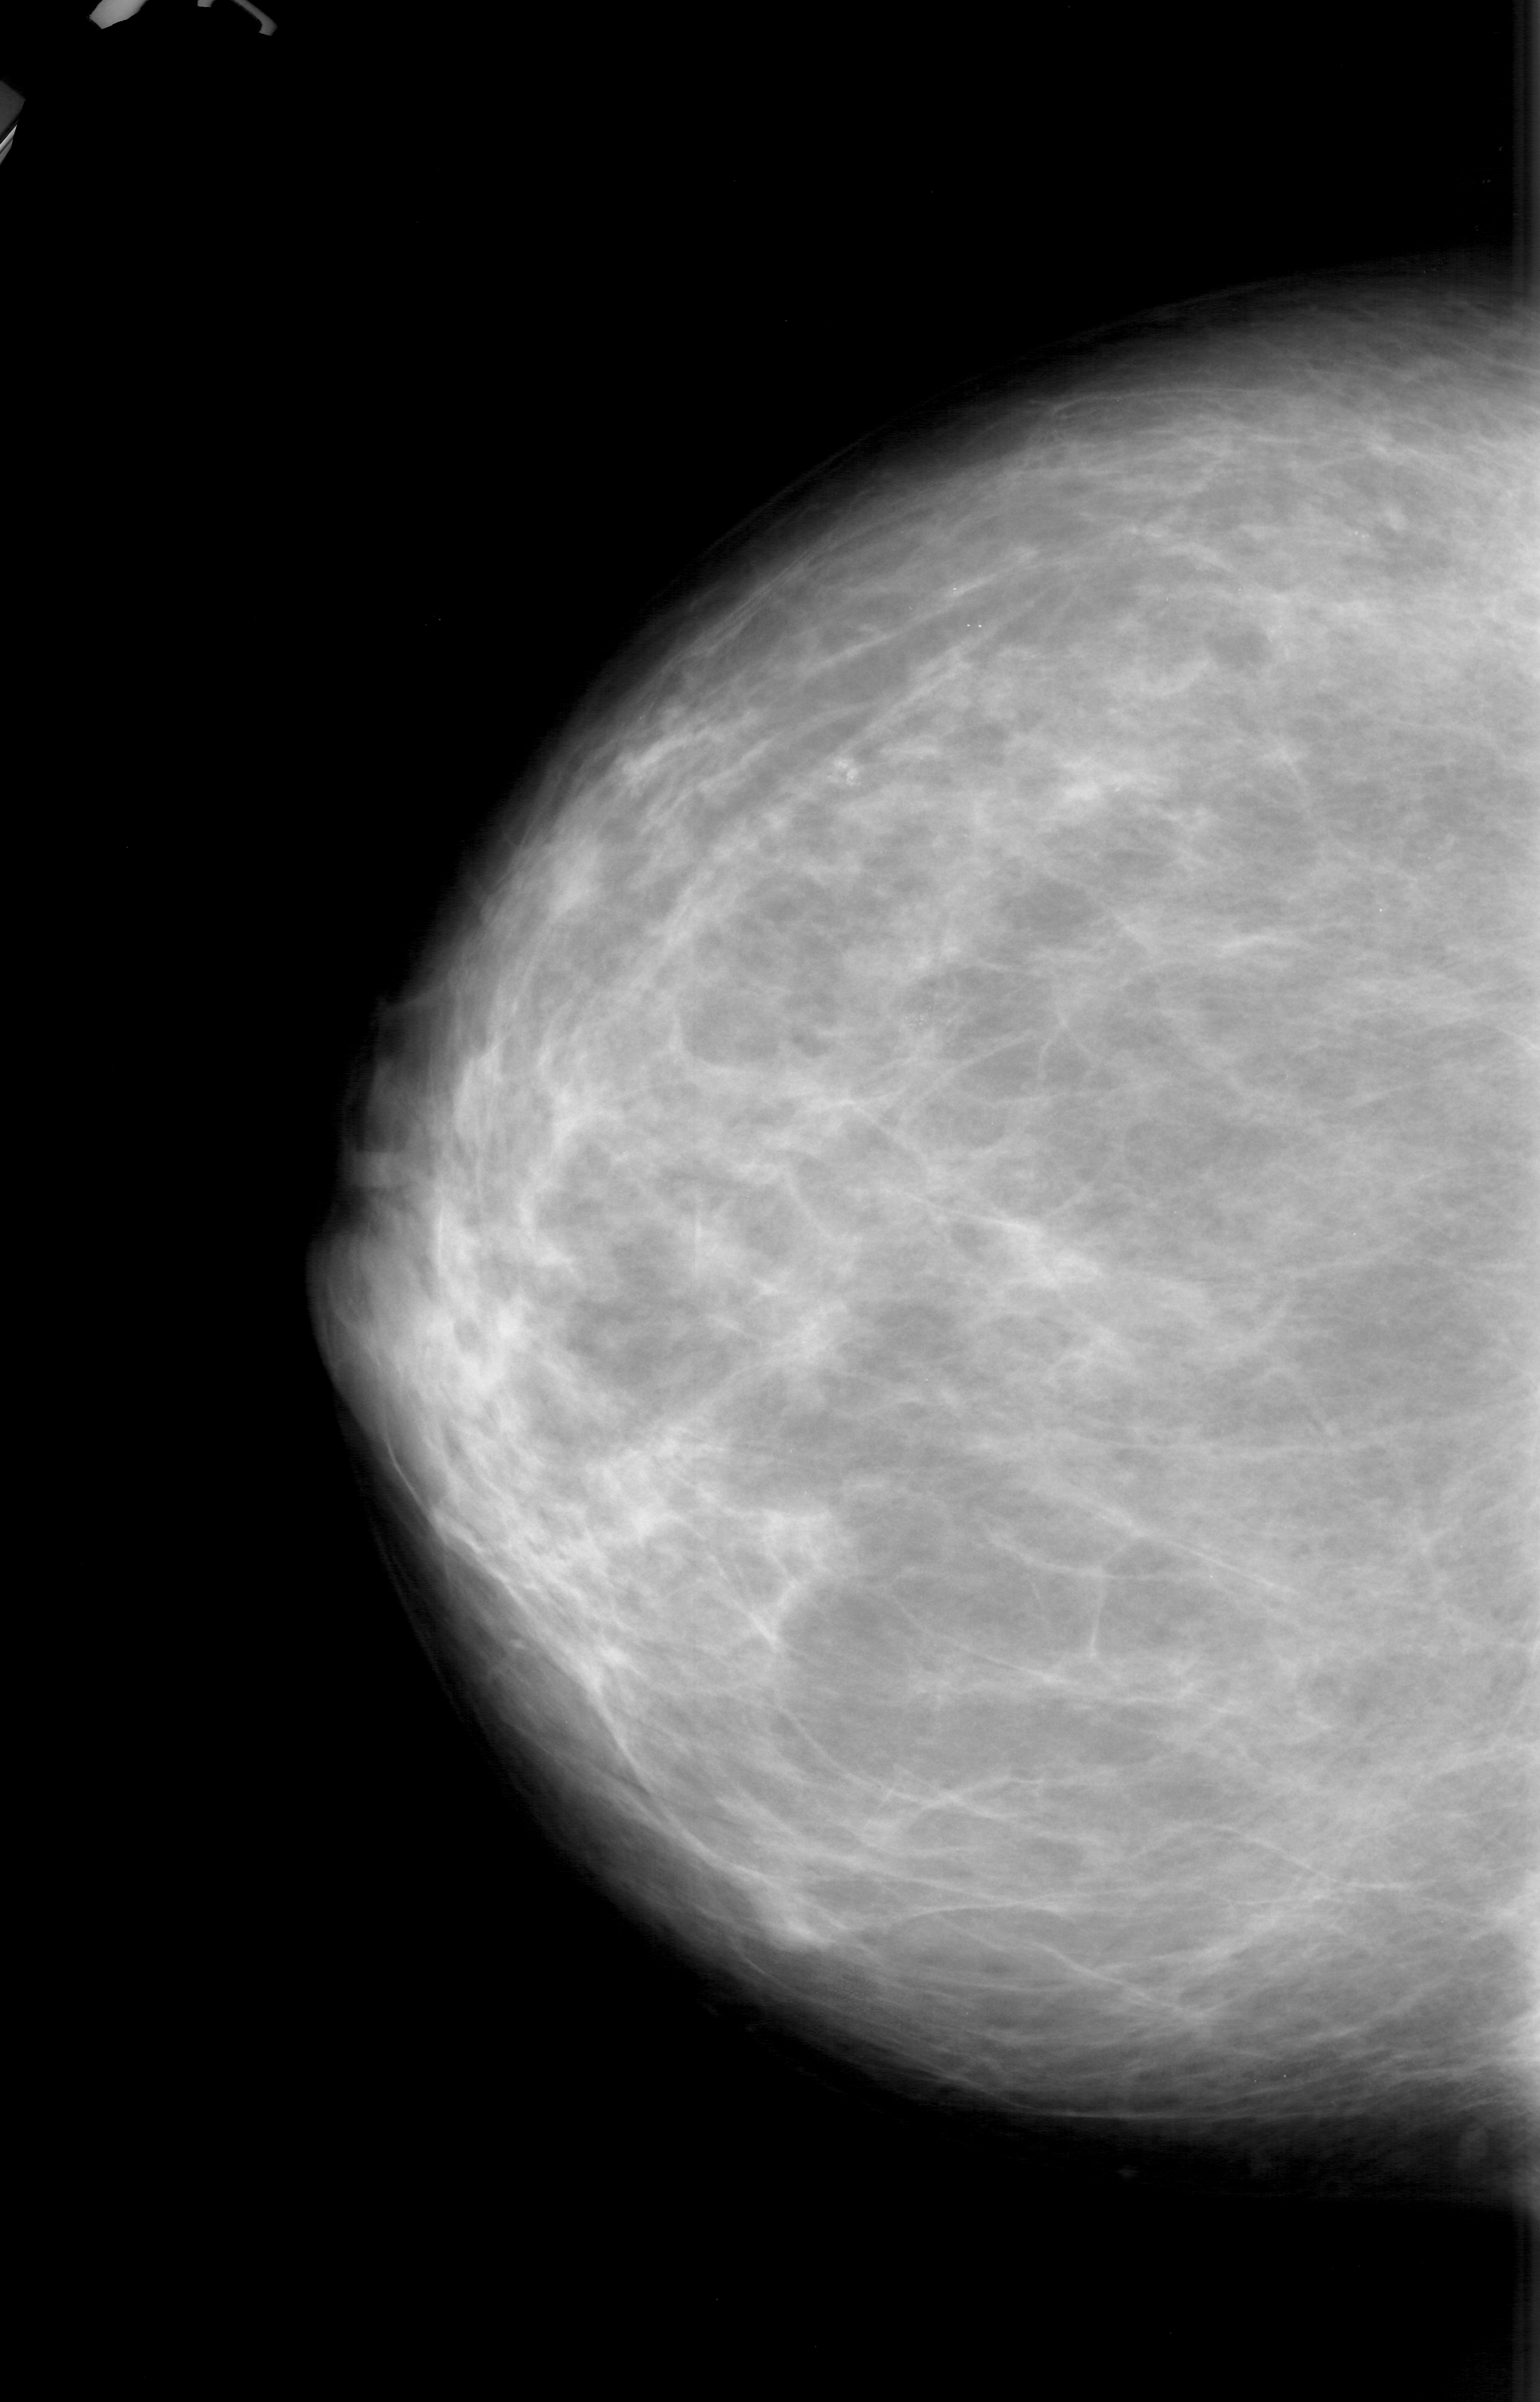
Digitized screen-film mammogram; left breast; craniocaudal (CC) view; 1540 × 2402 image matrix.
Expert-marked regions of interest on this film, with their recorded descriptors:
- calcifications, morphology pleomorphic, distribution clustered; BI-RADS assessment category 4; pathology result (as recorded, not read from the image): malignant: box from (x=824, y=927) to (x=1003, y=1101) px